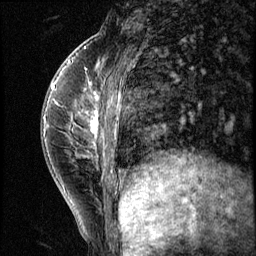
Breast MRI (dynamic contrast-enhanced), one sagittal slice; position 19 of 56 along the scan axis; 3 images stored at this slice position (order not interpretable as contrast timing); 1.5 T; TE 4.2 ms, TR 8.7 ms; 2.5 mm slice thickness; 256 × 256 image matrix. Female patient, age 35 years. Case-level facts recorded for this patient, not image findings: setting: breast cancer imaged before/during neoadjuvant chemotherapy; receptor status: HER2-positive.
Structures marked on this image (semi-automatic segmentation, software-assisted and operator-edited):
- analysis volume of interest (the breast-tissue region the enhancement analysis was run in; not a lesion): bounding box [x1, y1, x2, y2] px = [58, 84, 138, 186]
- tumour enhancement mask (voxels above the 140 % enhancement threshold inside the analysis volume of interest): [91, 92, 119, 172]